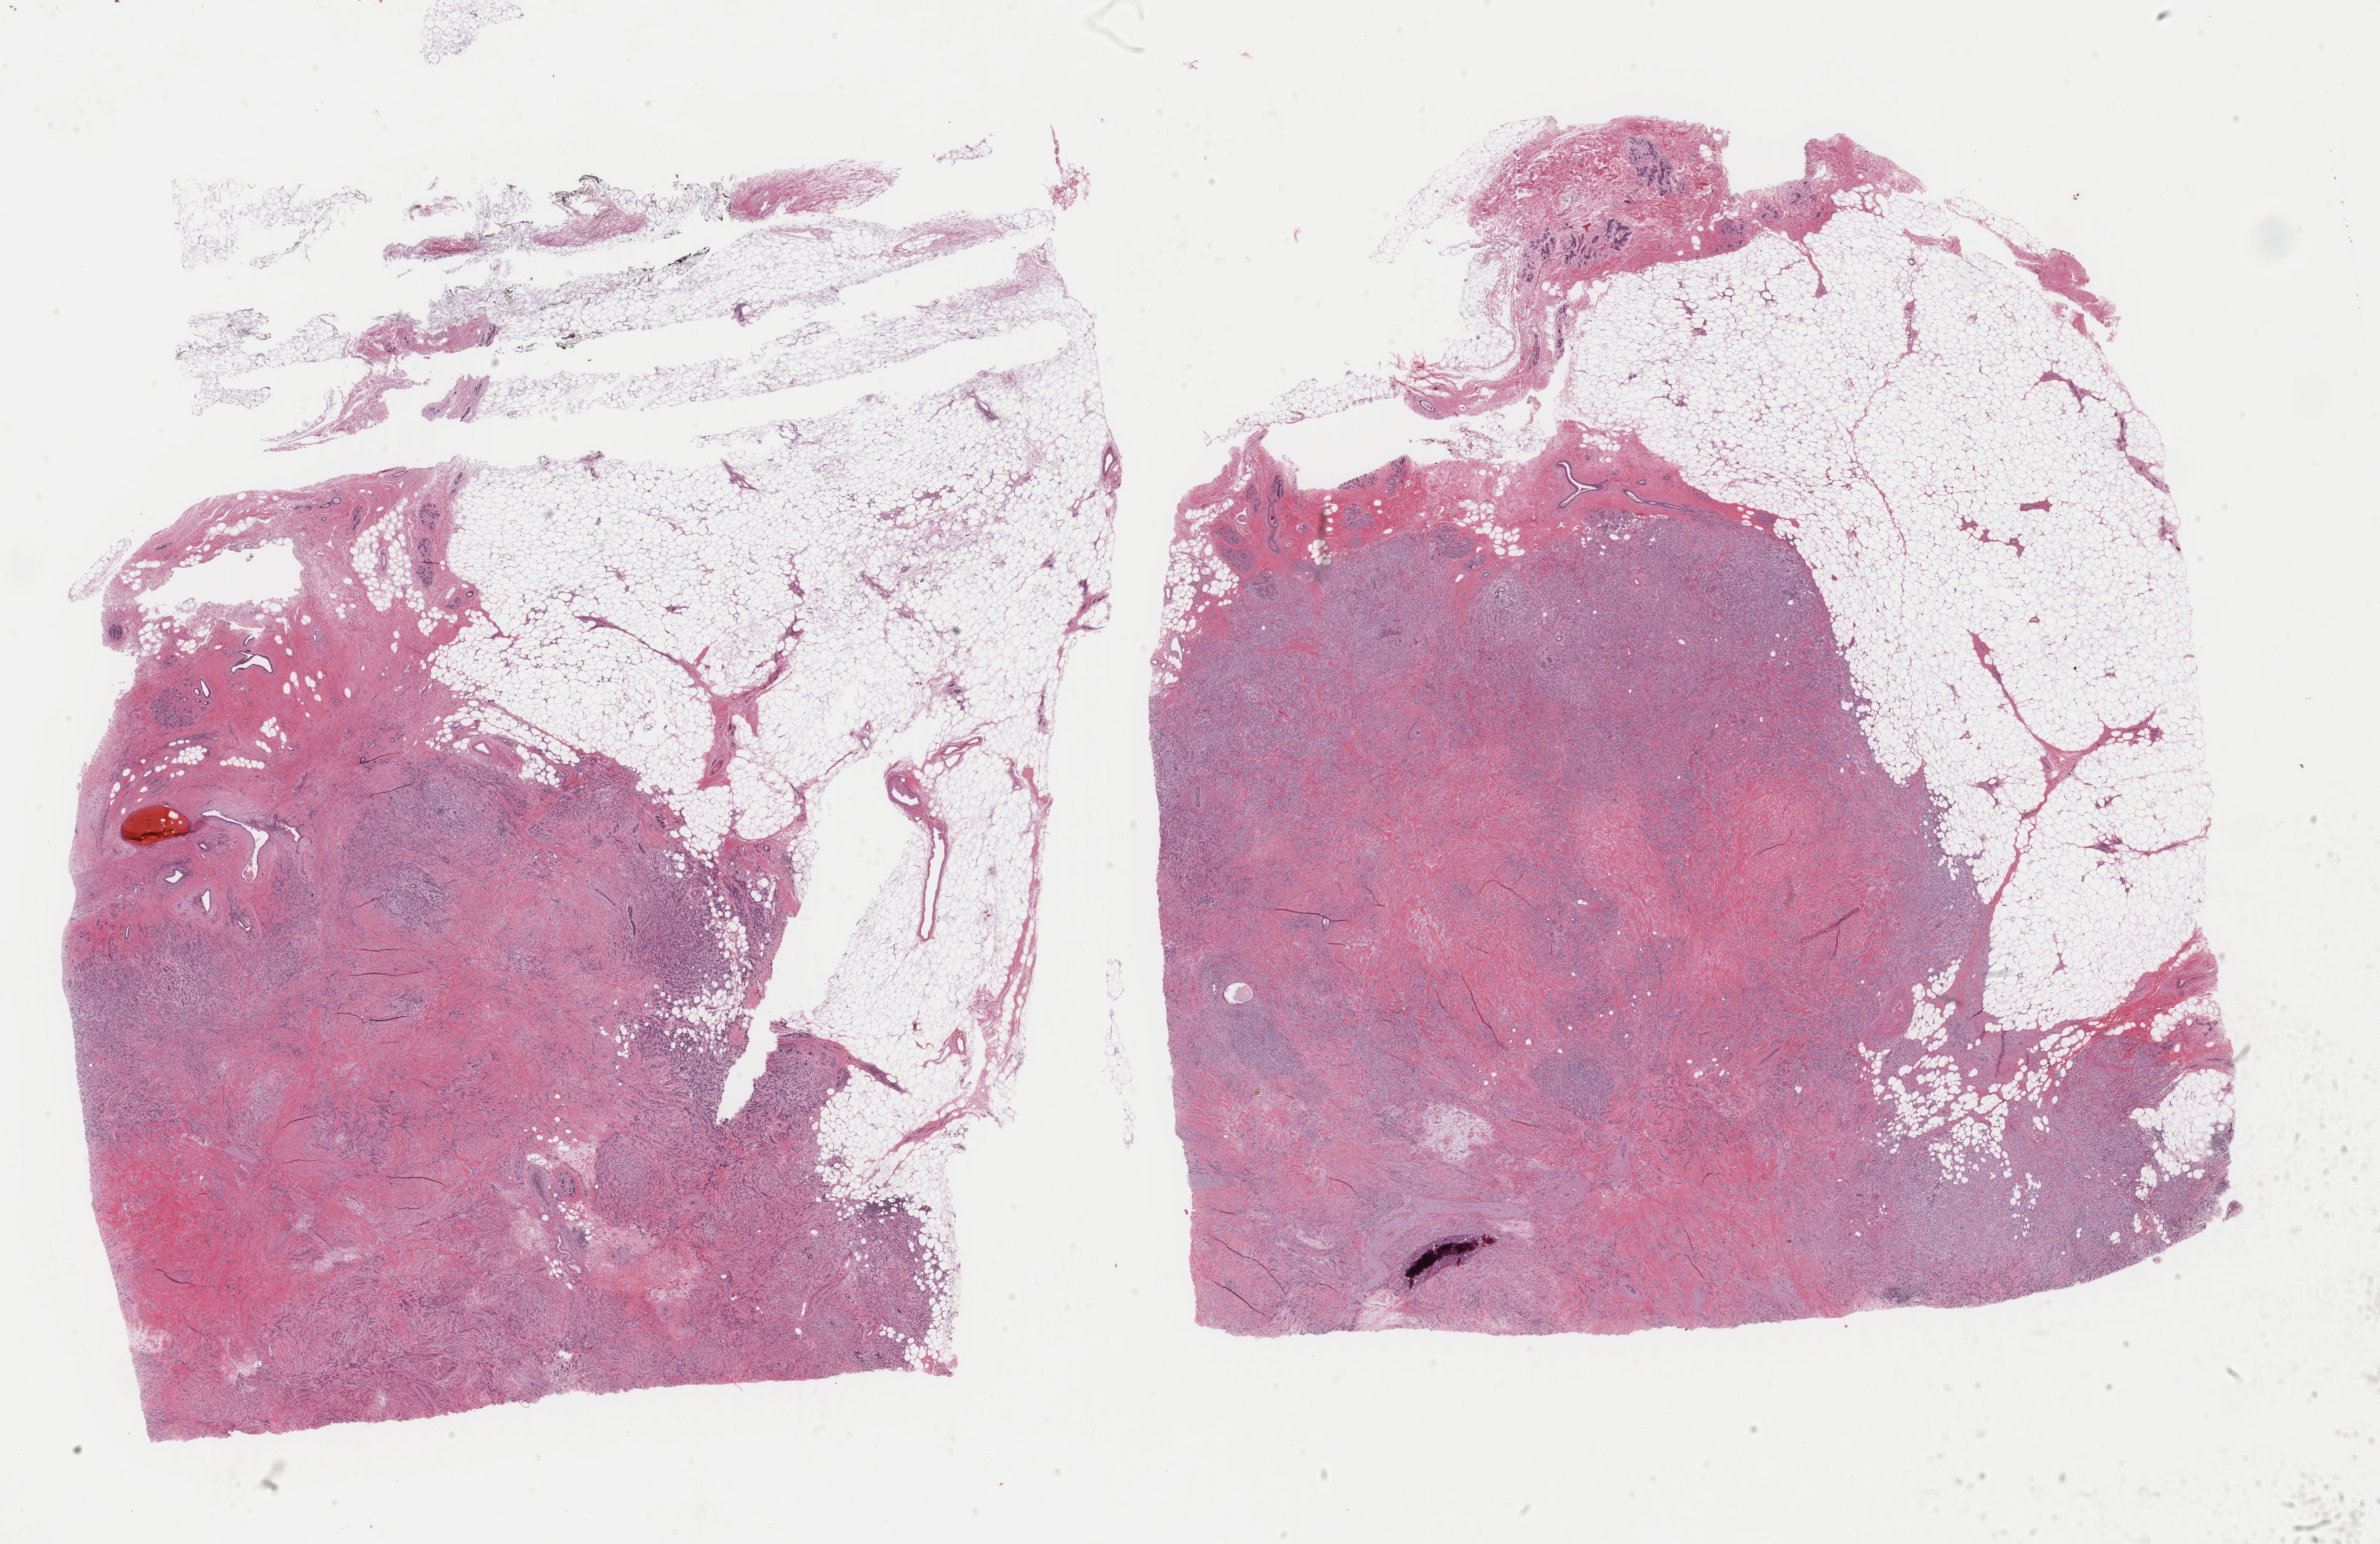
H&E whole-slide image — low-resolution overview of the scanned area, about 26.9 x 17.5 mm, formalin-fixed paraffin-embedded (FFPE) diagnostic section, primary tumour sample from the breast. Female, age 54 years at initial diagnosis.
- TNM: T2 N1 M0
- diagnosis: Lobular carcinoma, NOS
- lymph nodes positive (case pathology): 1 of 40 examined
- AJCC pathologic stage: IIB